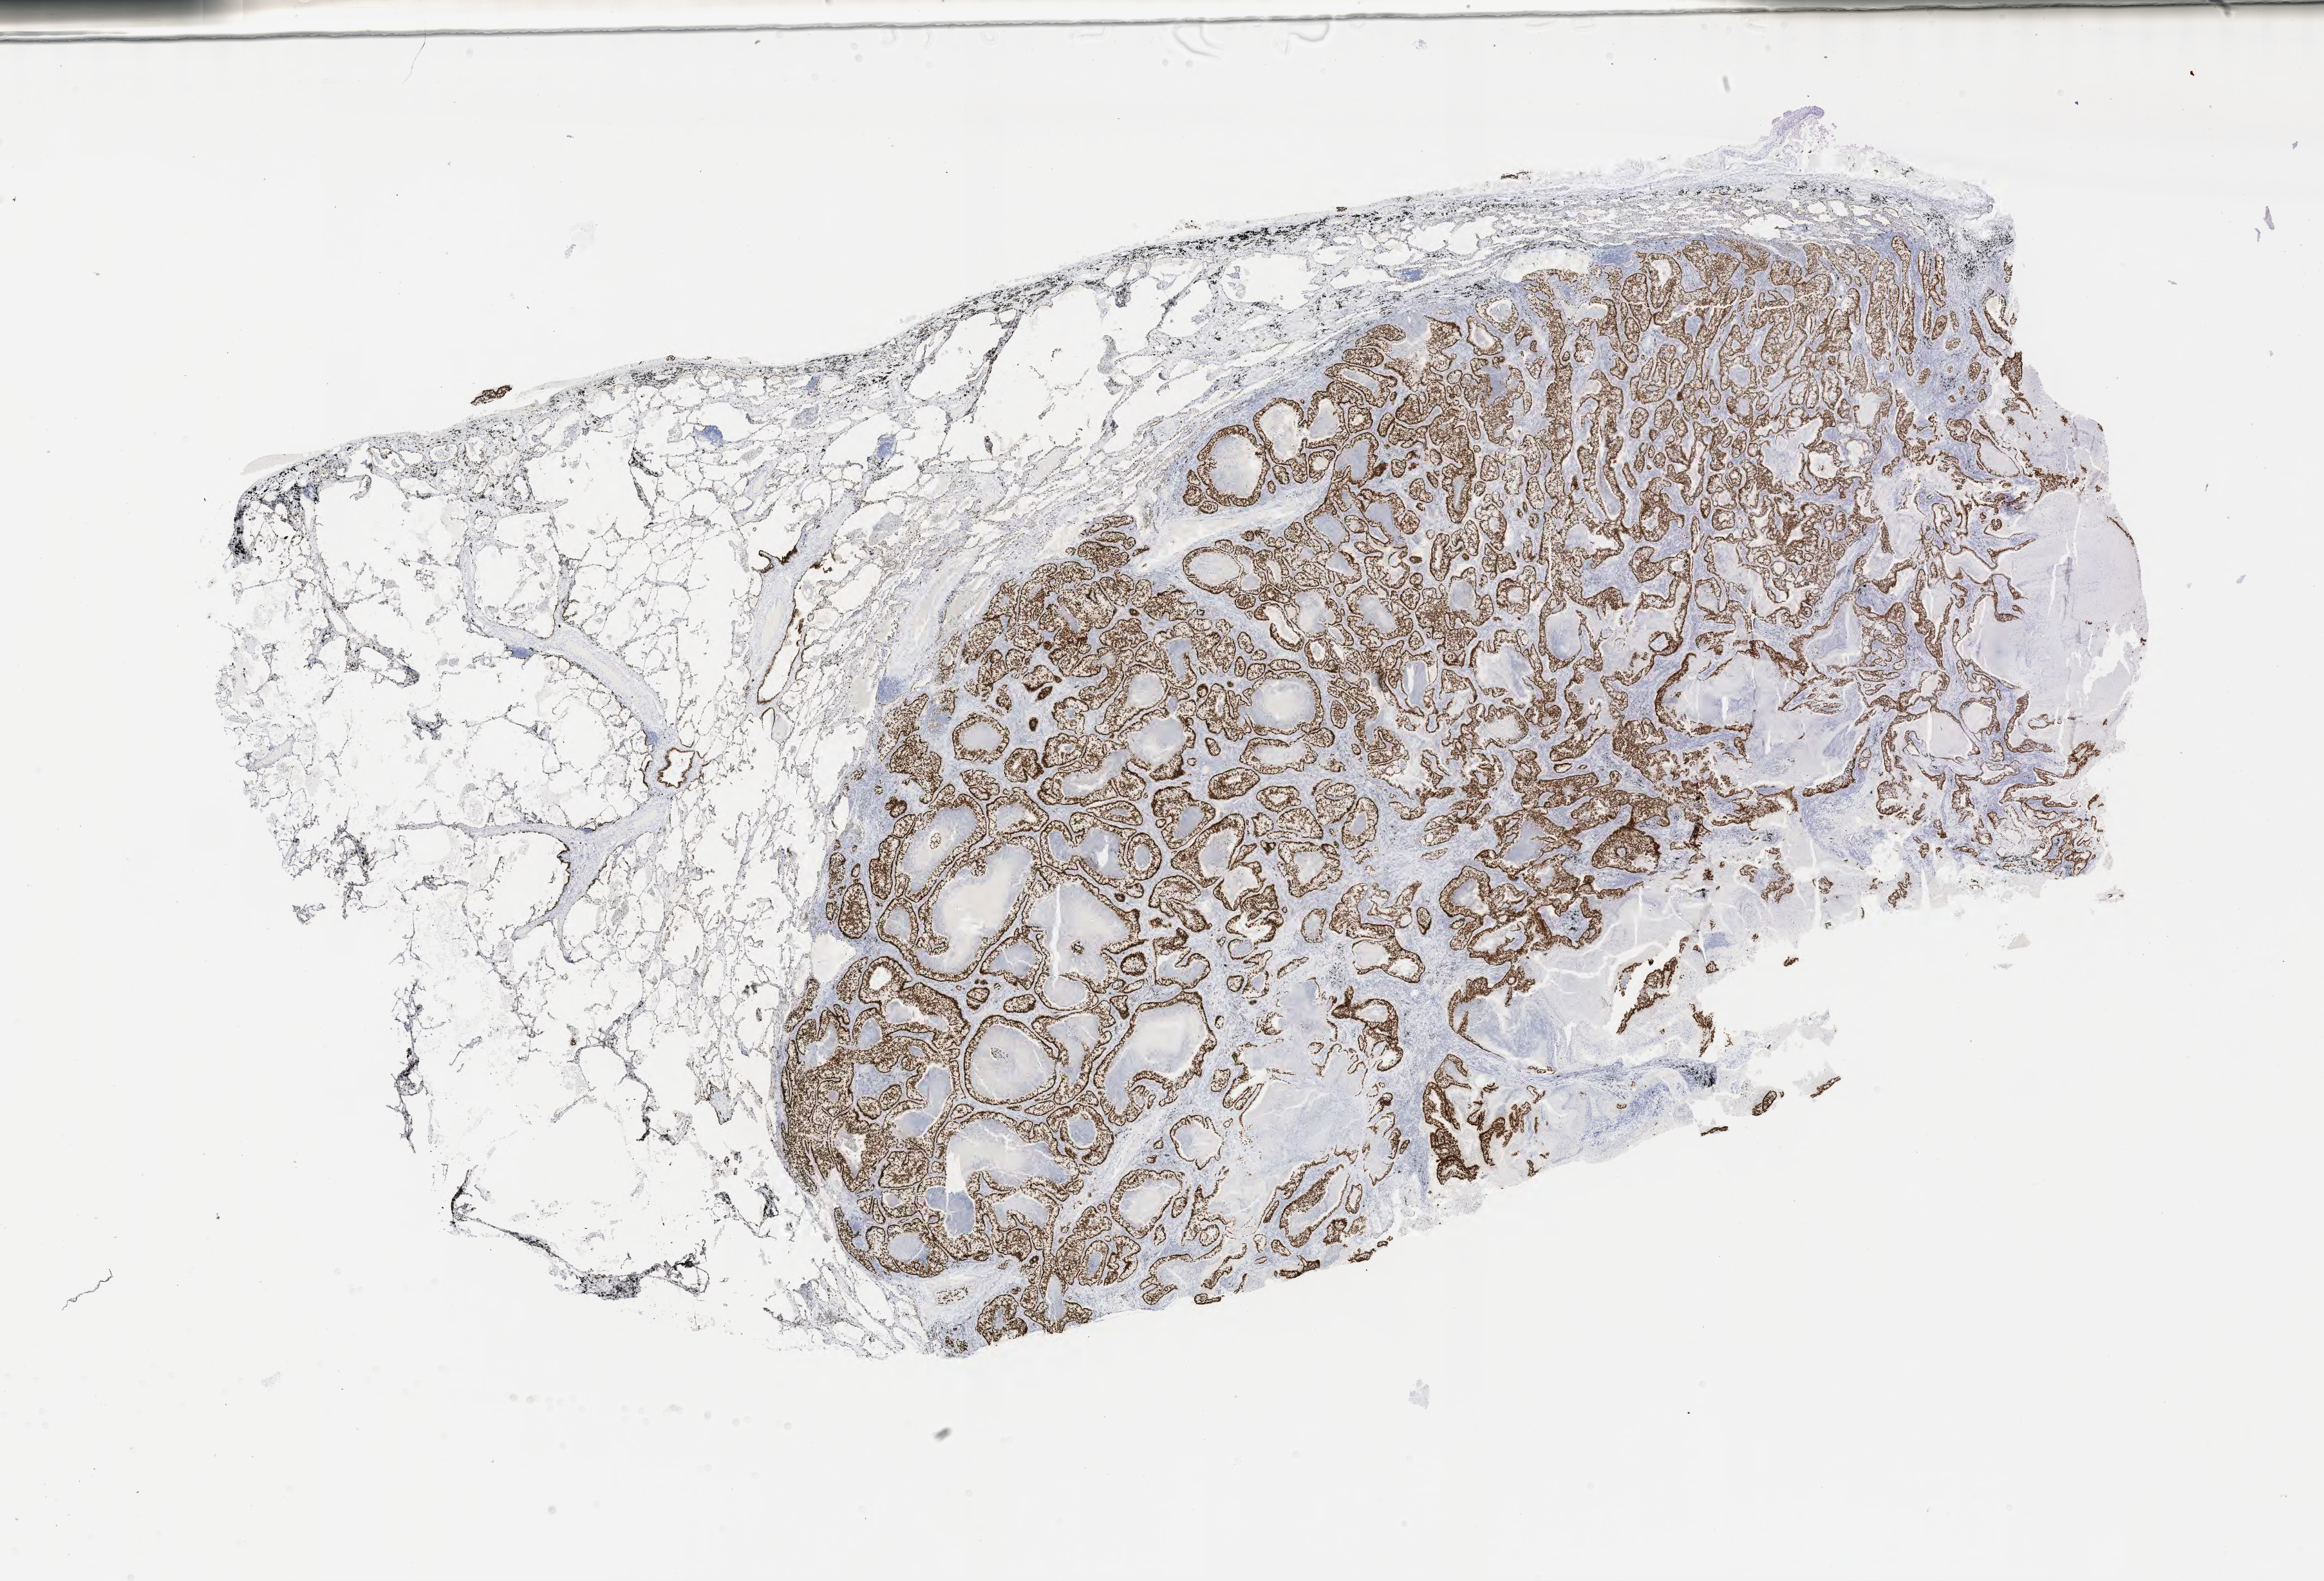
Whole-slide image, immunohistochemical stain for TTF-1 (thyroid transcription factor 1), whole scanned area (about 29.2 x 19.8 mm) shown as a low-resolution overview. Tumor tissue. Site: lung. Female patient.
Histologic diagnosis: Adenocarcinoma, NOS.